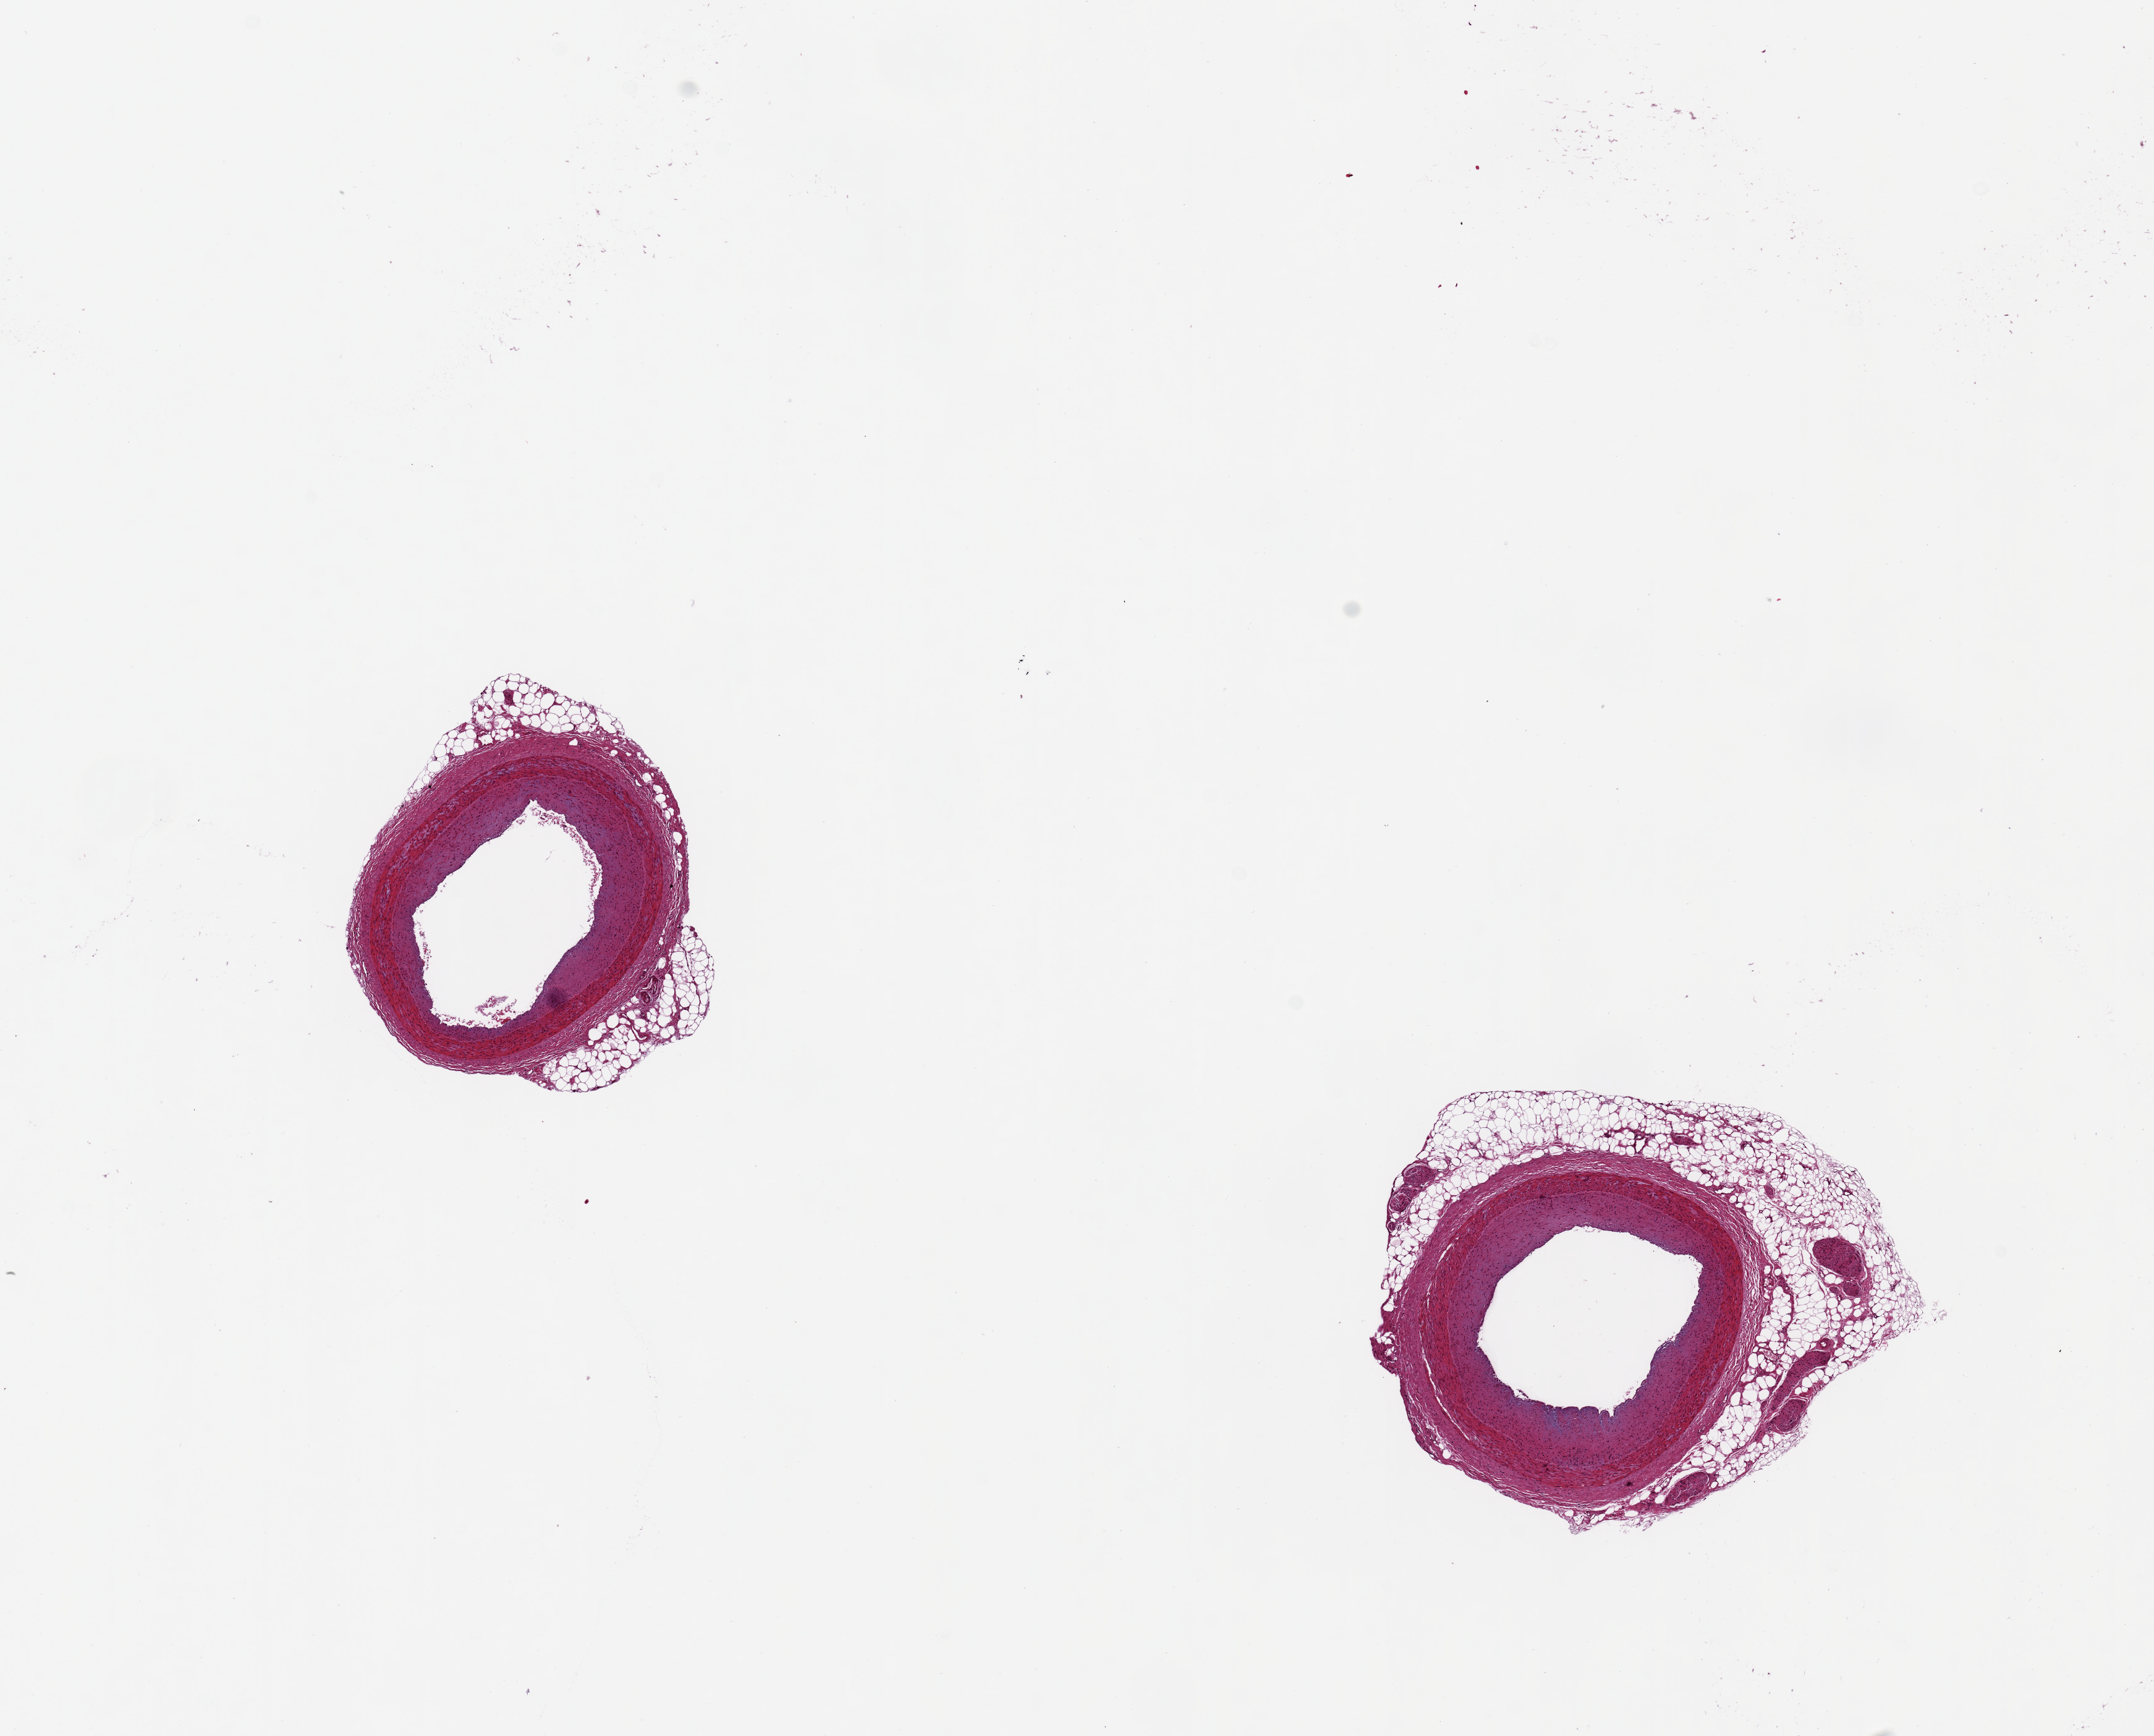
Whole-slide image, haematoxylin and eosin stain, brightfield — shown as a low-resolution overview of the whole scanned area (about 13.8 x 11.1 mm). PAXgene-fixed, paraffin-embedded tissue. Section of coronary artery (target tissue). Donor tissue sample. Donor: male.
Reviewer comment on this tissue sample: 2 pieces ~2mm d. Discontinuous rims of fat on both, up to 0.5mm. Minimal atherosis.